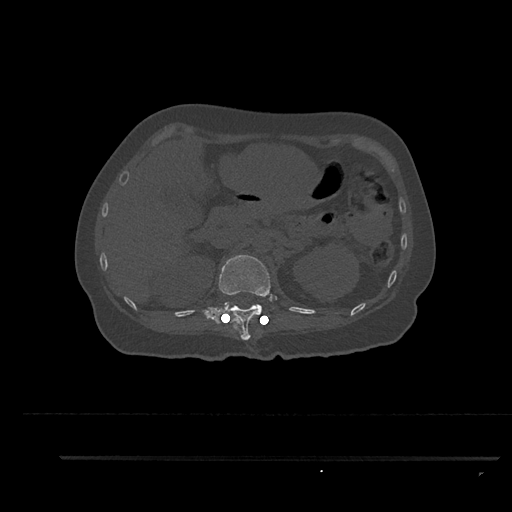
CT including the spine, one axial slice; slice 249 of 797 in the series (ordered by position); reconstruction kernel Br40s/3; bone window (W 1800 / L 400 HU); 0.5 mm slice thickness; 512 × 512 image matrix, field of view 408 × 408 mm. Patient: female, 44 years. From the clinical record (not read from this slice): primary cancer: renal.
Annotated regions visible in this slice (semi-automatic segmentation, software-assisted and operator-edited):
- T12 vertebra: bounding box (x1, y1, x2, y2) in pixels: (200, 255, 273, 340)